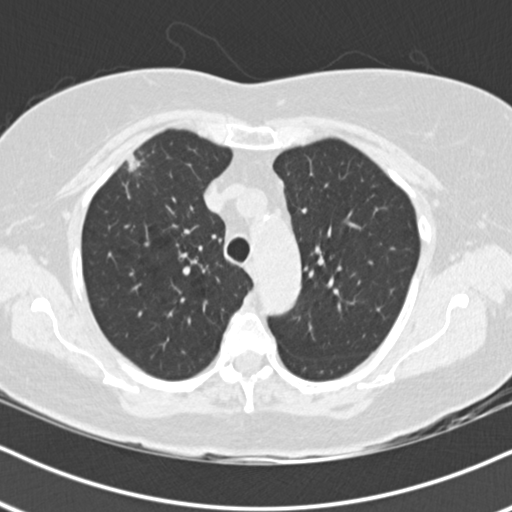
Axial slice from a low-dose chest CT screening exam, first (baseline) screen, lung window (W 1500 / L -600 HU), 2 mm slice thickness, standard (soft-tissue) reconstruction kernel (B30f), 120 kVp. Female participant, aged 74 years at enrolment.
Lesion marked by an expert reader, bounding box (x1, y1, x2, y2) in pixels: (105, 138, 159, 193). The exam's reader record, not a measurement of the box and not confirmed to be the same lesion: non-calcified nodule or mass ≥4 mm, right upper lobe, 16 × 10 mm, poorly defined margins, soft tissue attenuation. Later outcome: lung cancer diagnosed 33 days after this screen — adenocarcinoma, NOS, right upper lobe, poorly differentiated (G3), stage IIIA (AJCC 6th edition), 24 mm at pathology.